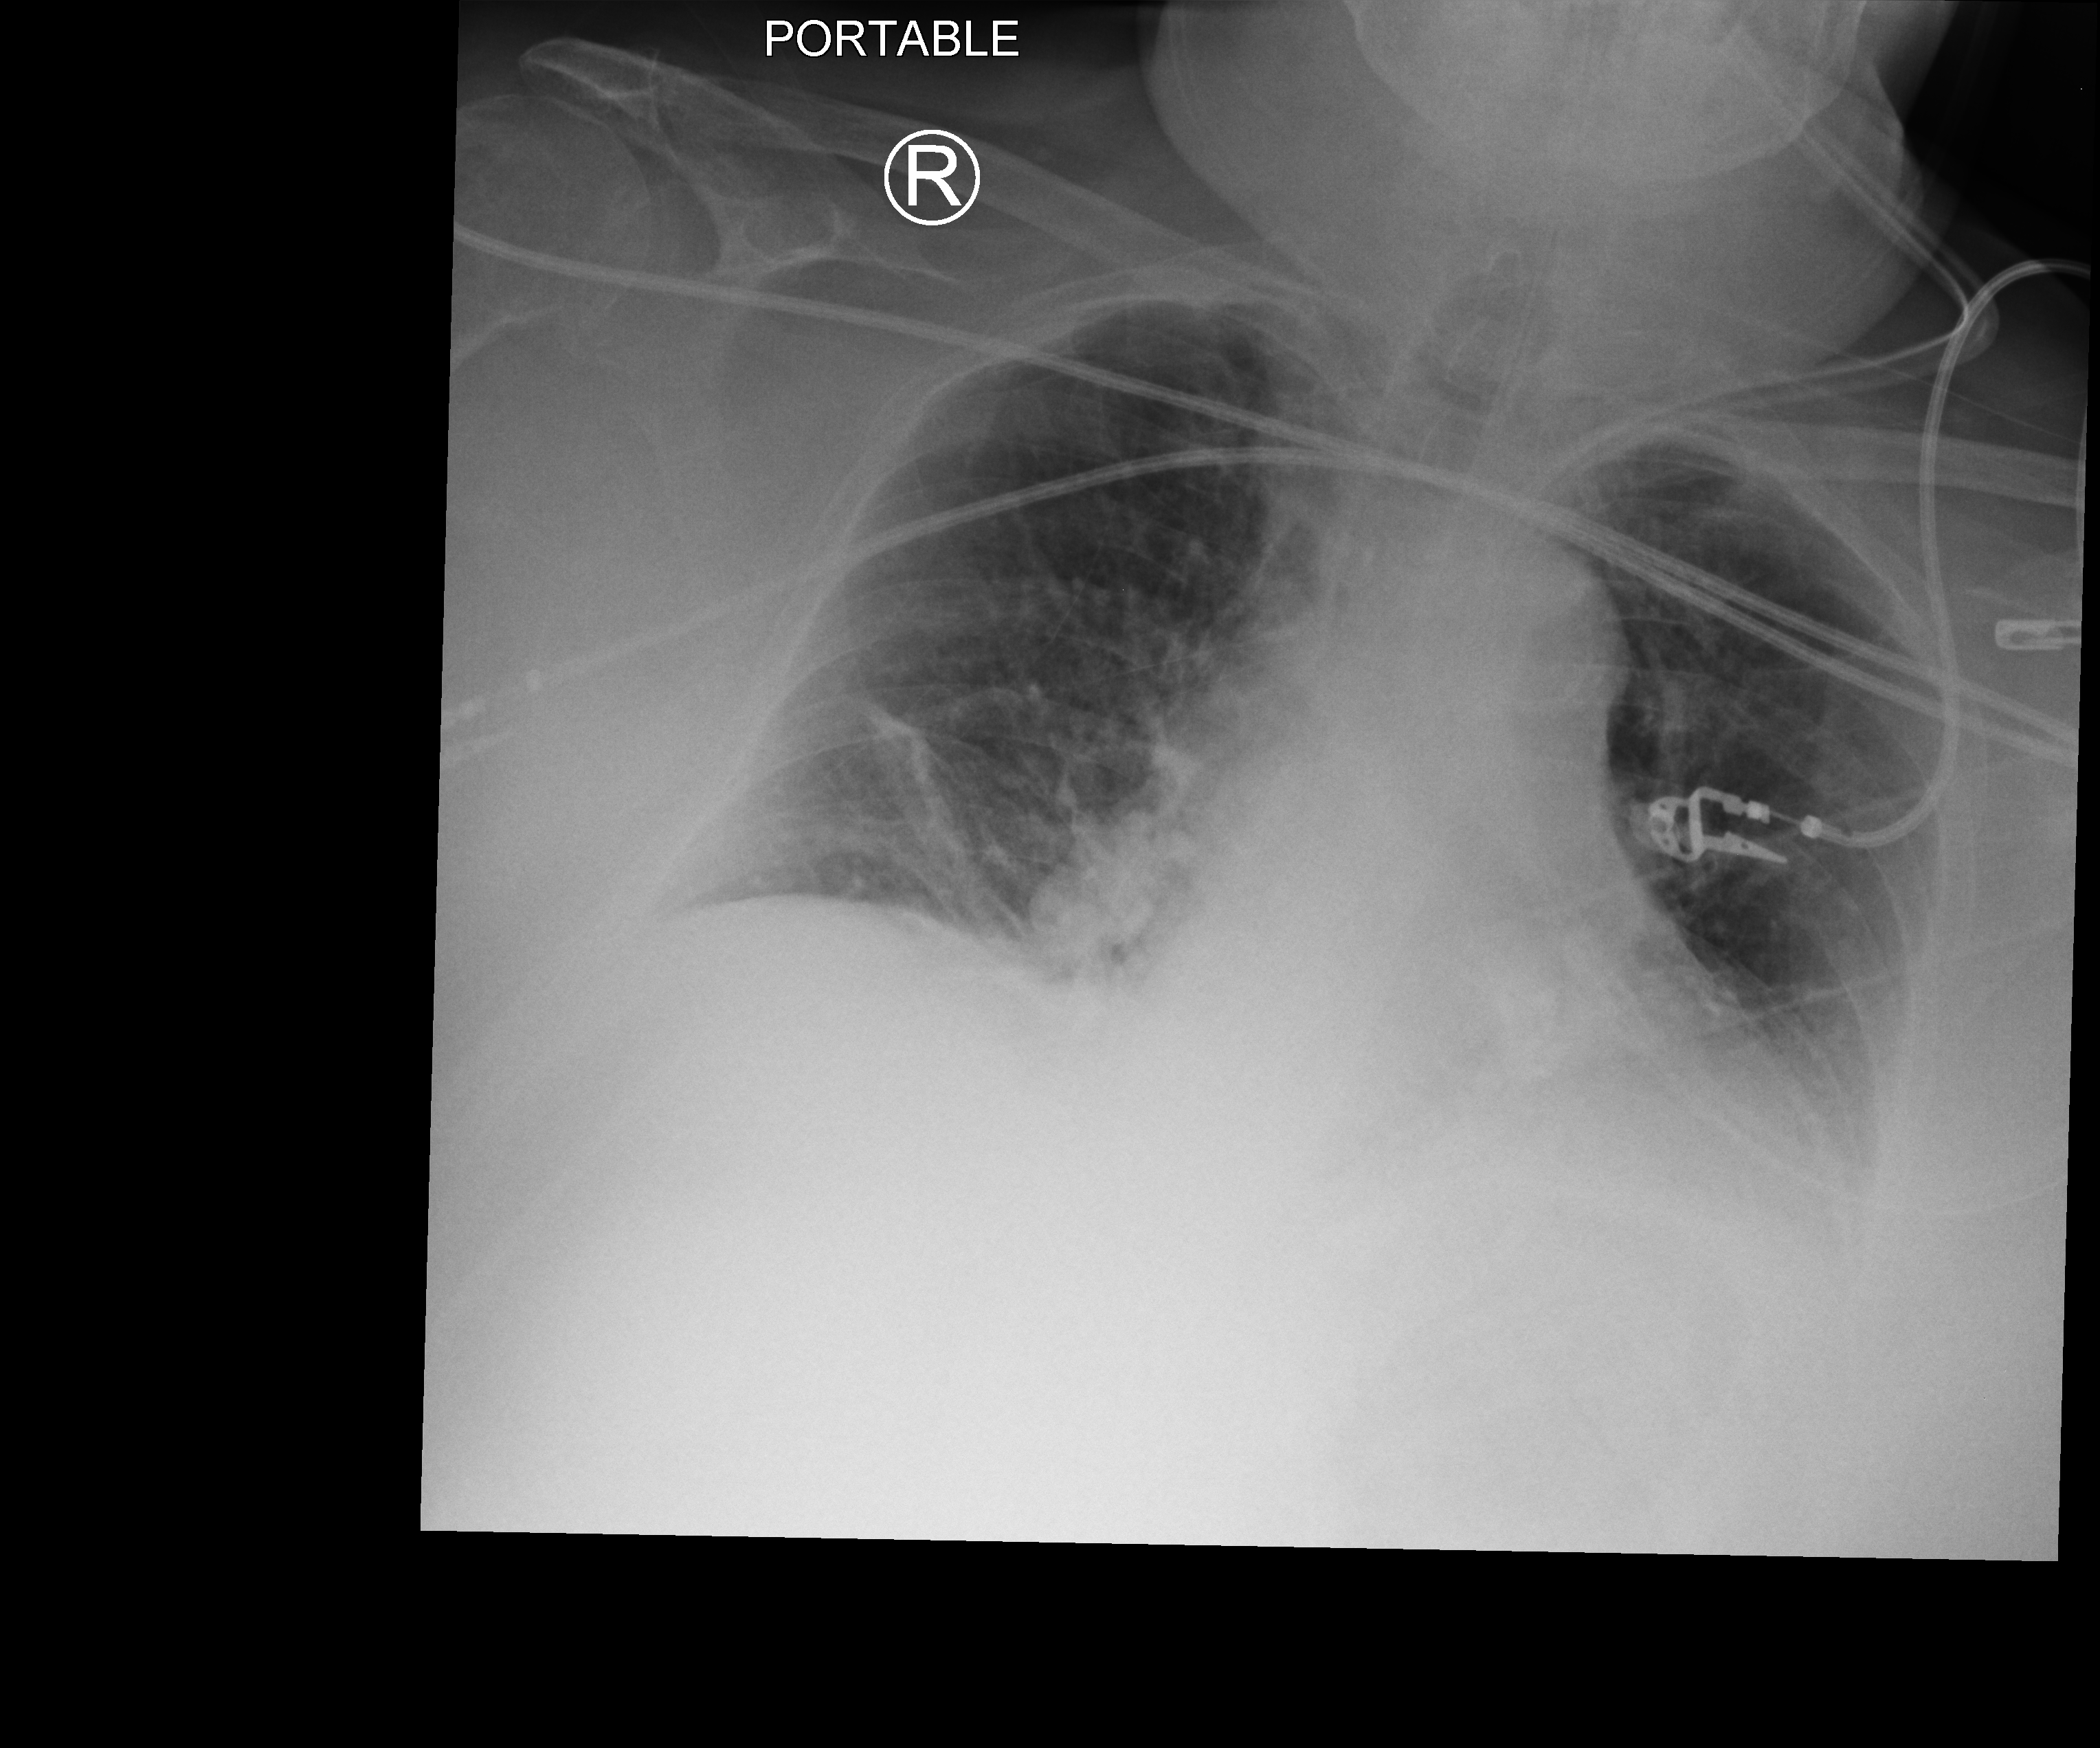
Portable chest radiograph. Patient hospitalised with COVID-19; female, aged 60–74 years.
Admission-level facts for this patient (not findings on this image; timing relative to this image not recorded):
- admitted to intensive care during this hospital stay: yes